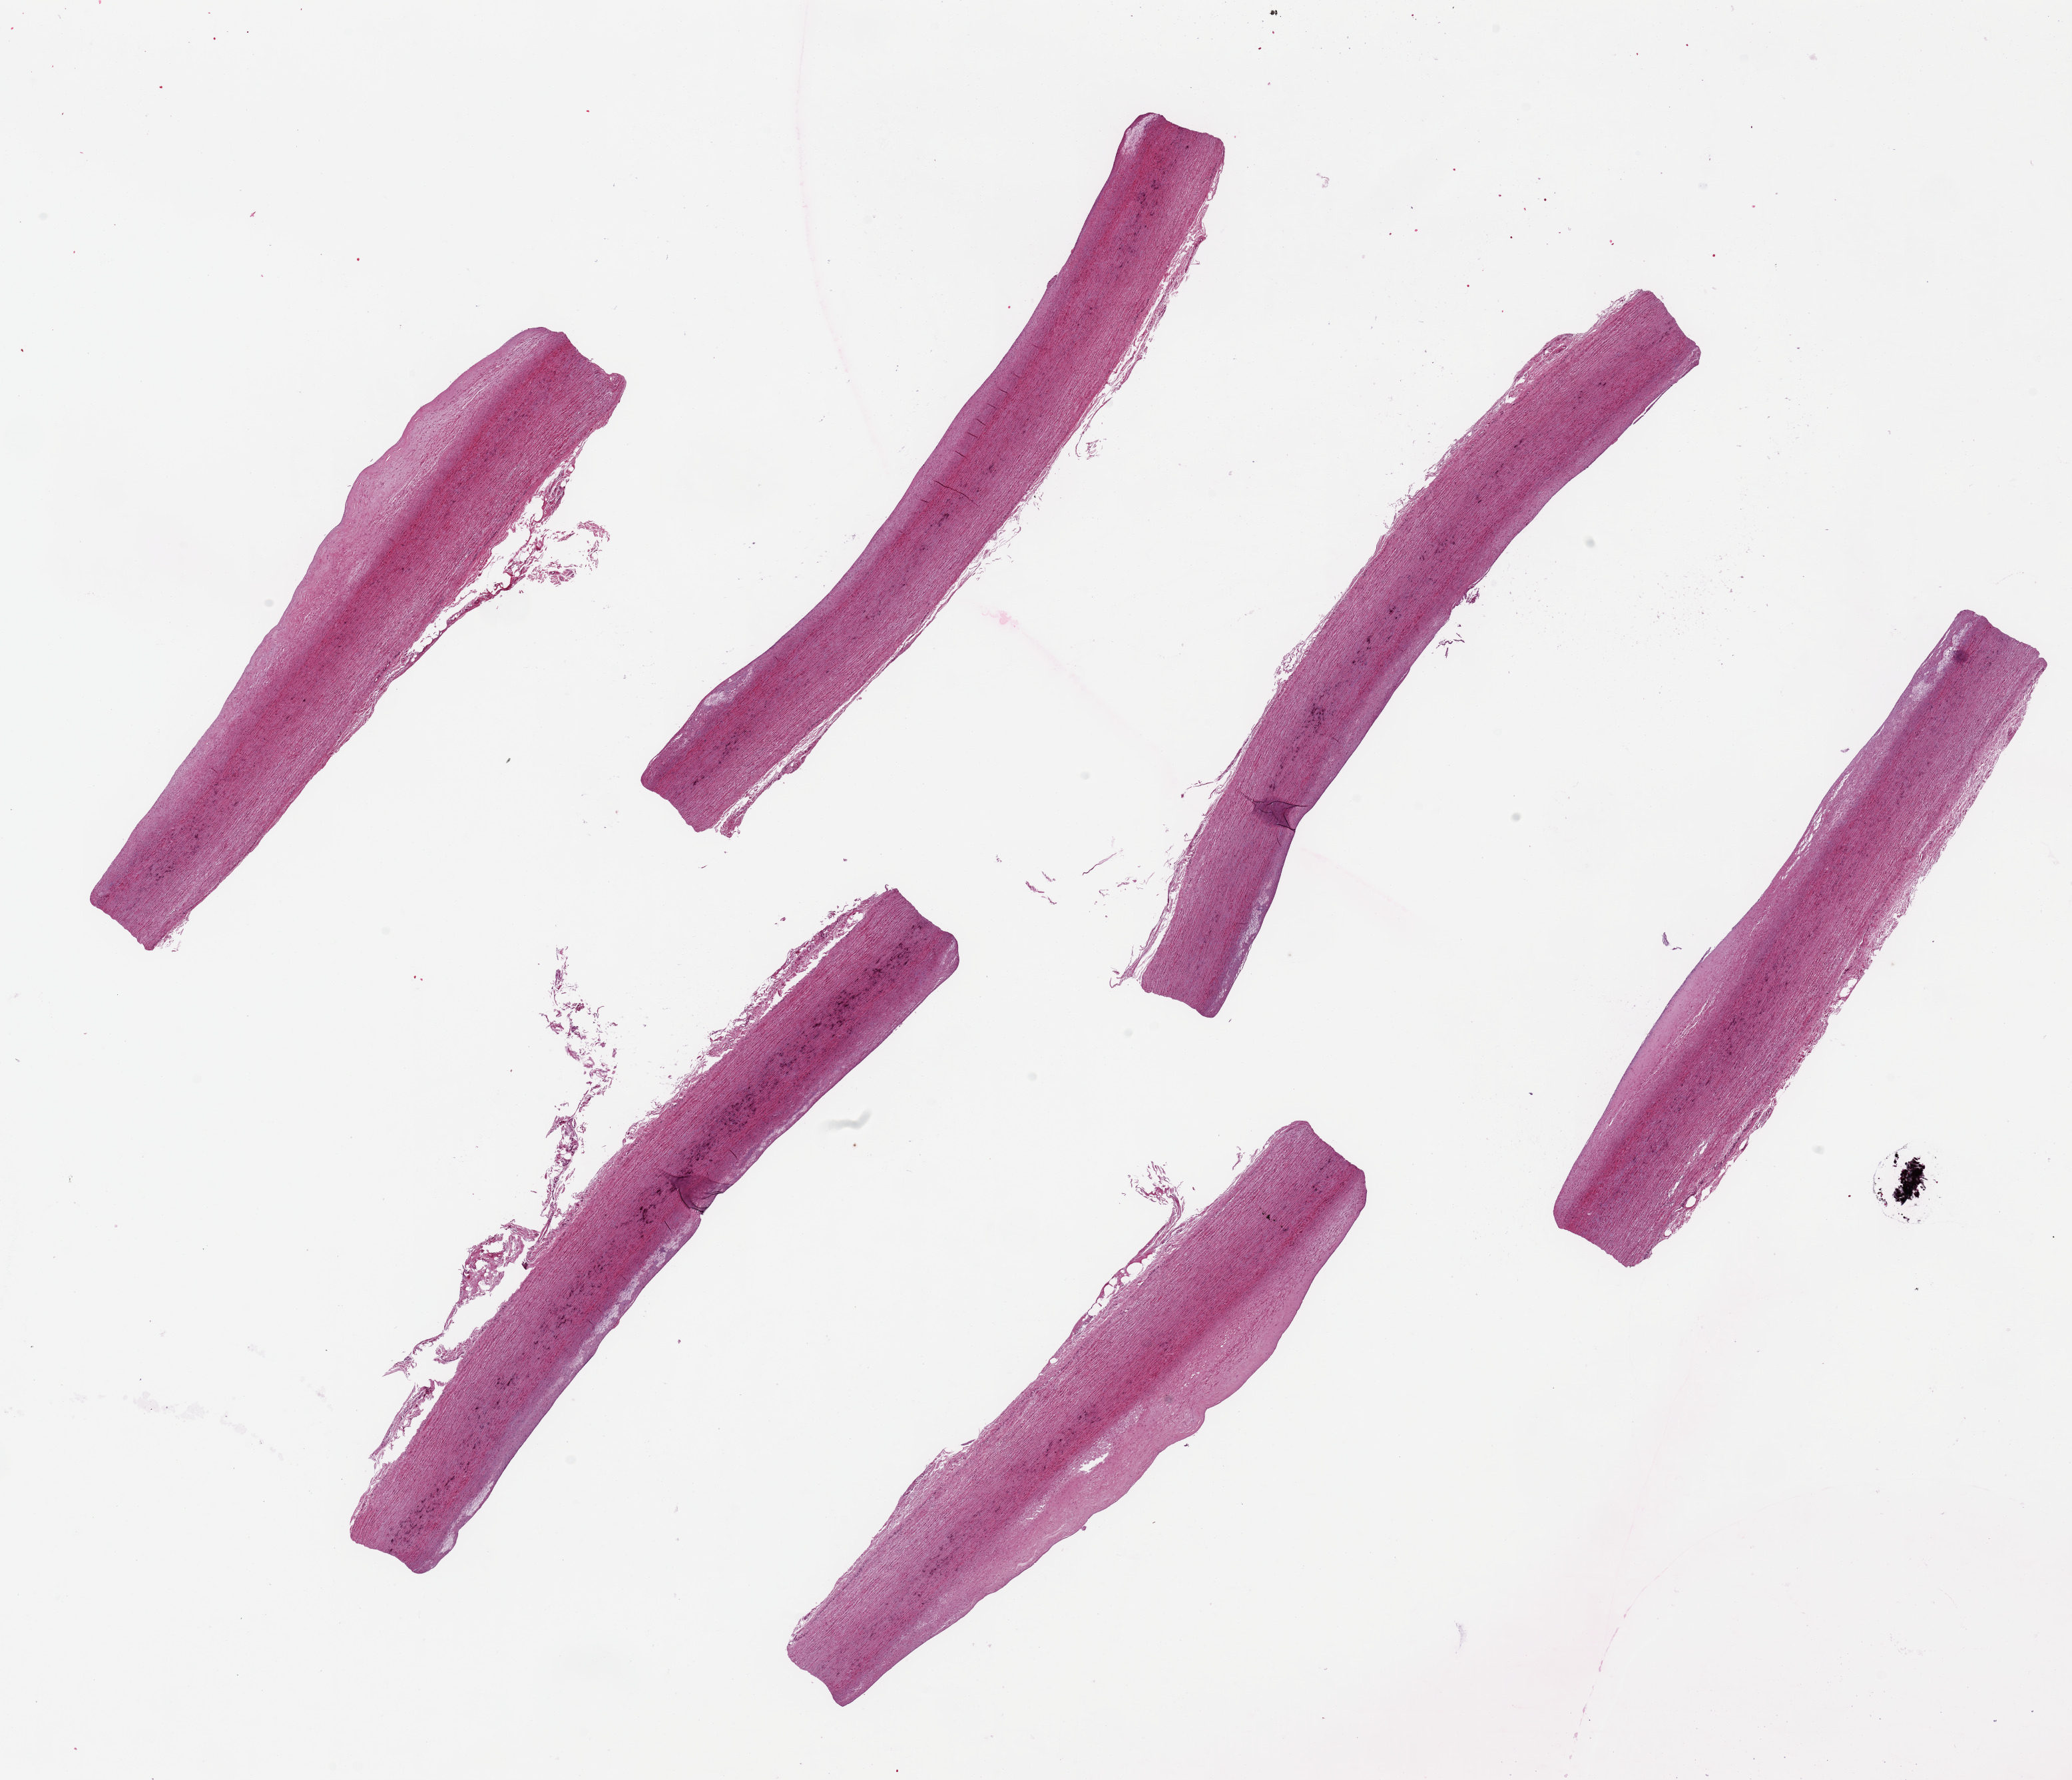
Digitized hematoxylin and eosin (H&E)-stained section, whole scanned area (about 24.6 x 21.1 mm, acquisition: 20x scan) shown as a low-resolution overview. PAXgene-fixed paraffin-embedded (PFPE) section. Sampled site (target tissue): aorta. Tissue donor sample.
Pathologist's review note for this sample: 6 pieces, up to 10x1mm; flat atherosclerotic plaques; clean of periaortic adipose.